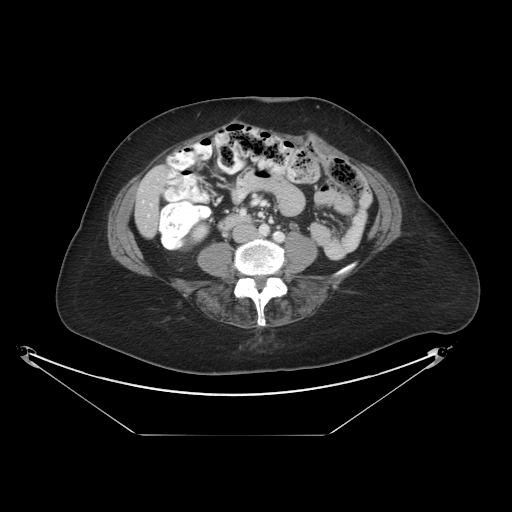
Contrast-enhanced abdominal CT, one axial slice; 120 kVp; intravenous contrast given; soft-tissue window (W 400 / L 40 HU); 5 mm slice thickness; 512 × 512 image matrix, field of view 500 × 500 mm. Female patient, age 70 years. Case-level facts recorded for this patient, not image findings: diagnosis: colorectal cancer liver metastases, imaged before liver resection; multiple liver metastases: no; largest metastasis: 2.5 cm; chemotherapy before resection: no.
Structures marked on this image (manually delineated by an expert):
- liver: bounding box (x1, y1, x2, y2) in pixels: (136, 167, 167, 236)